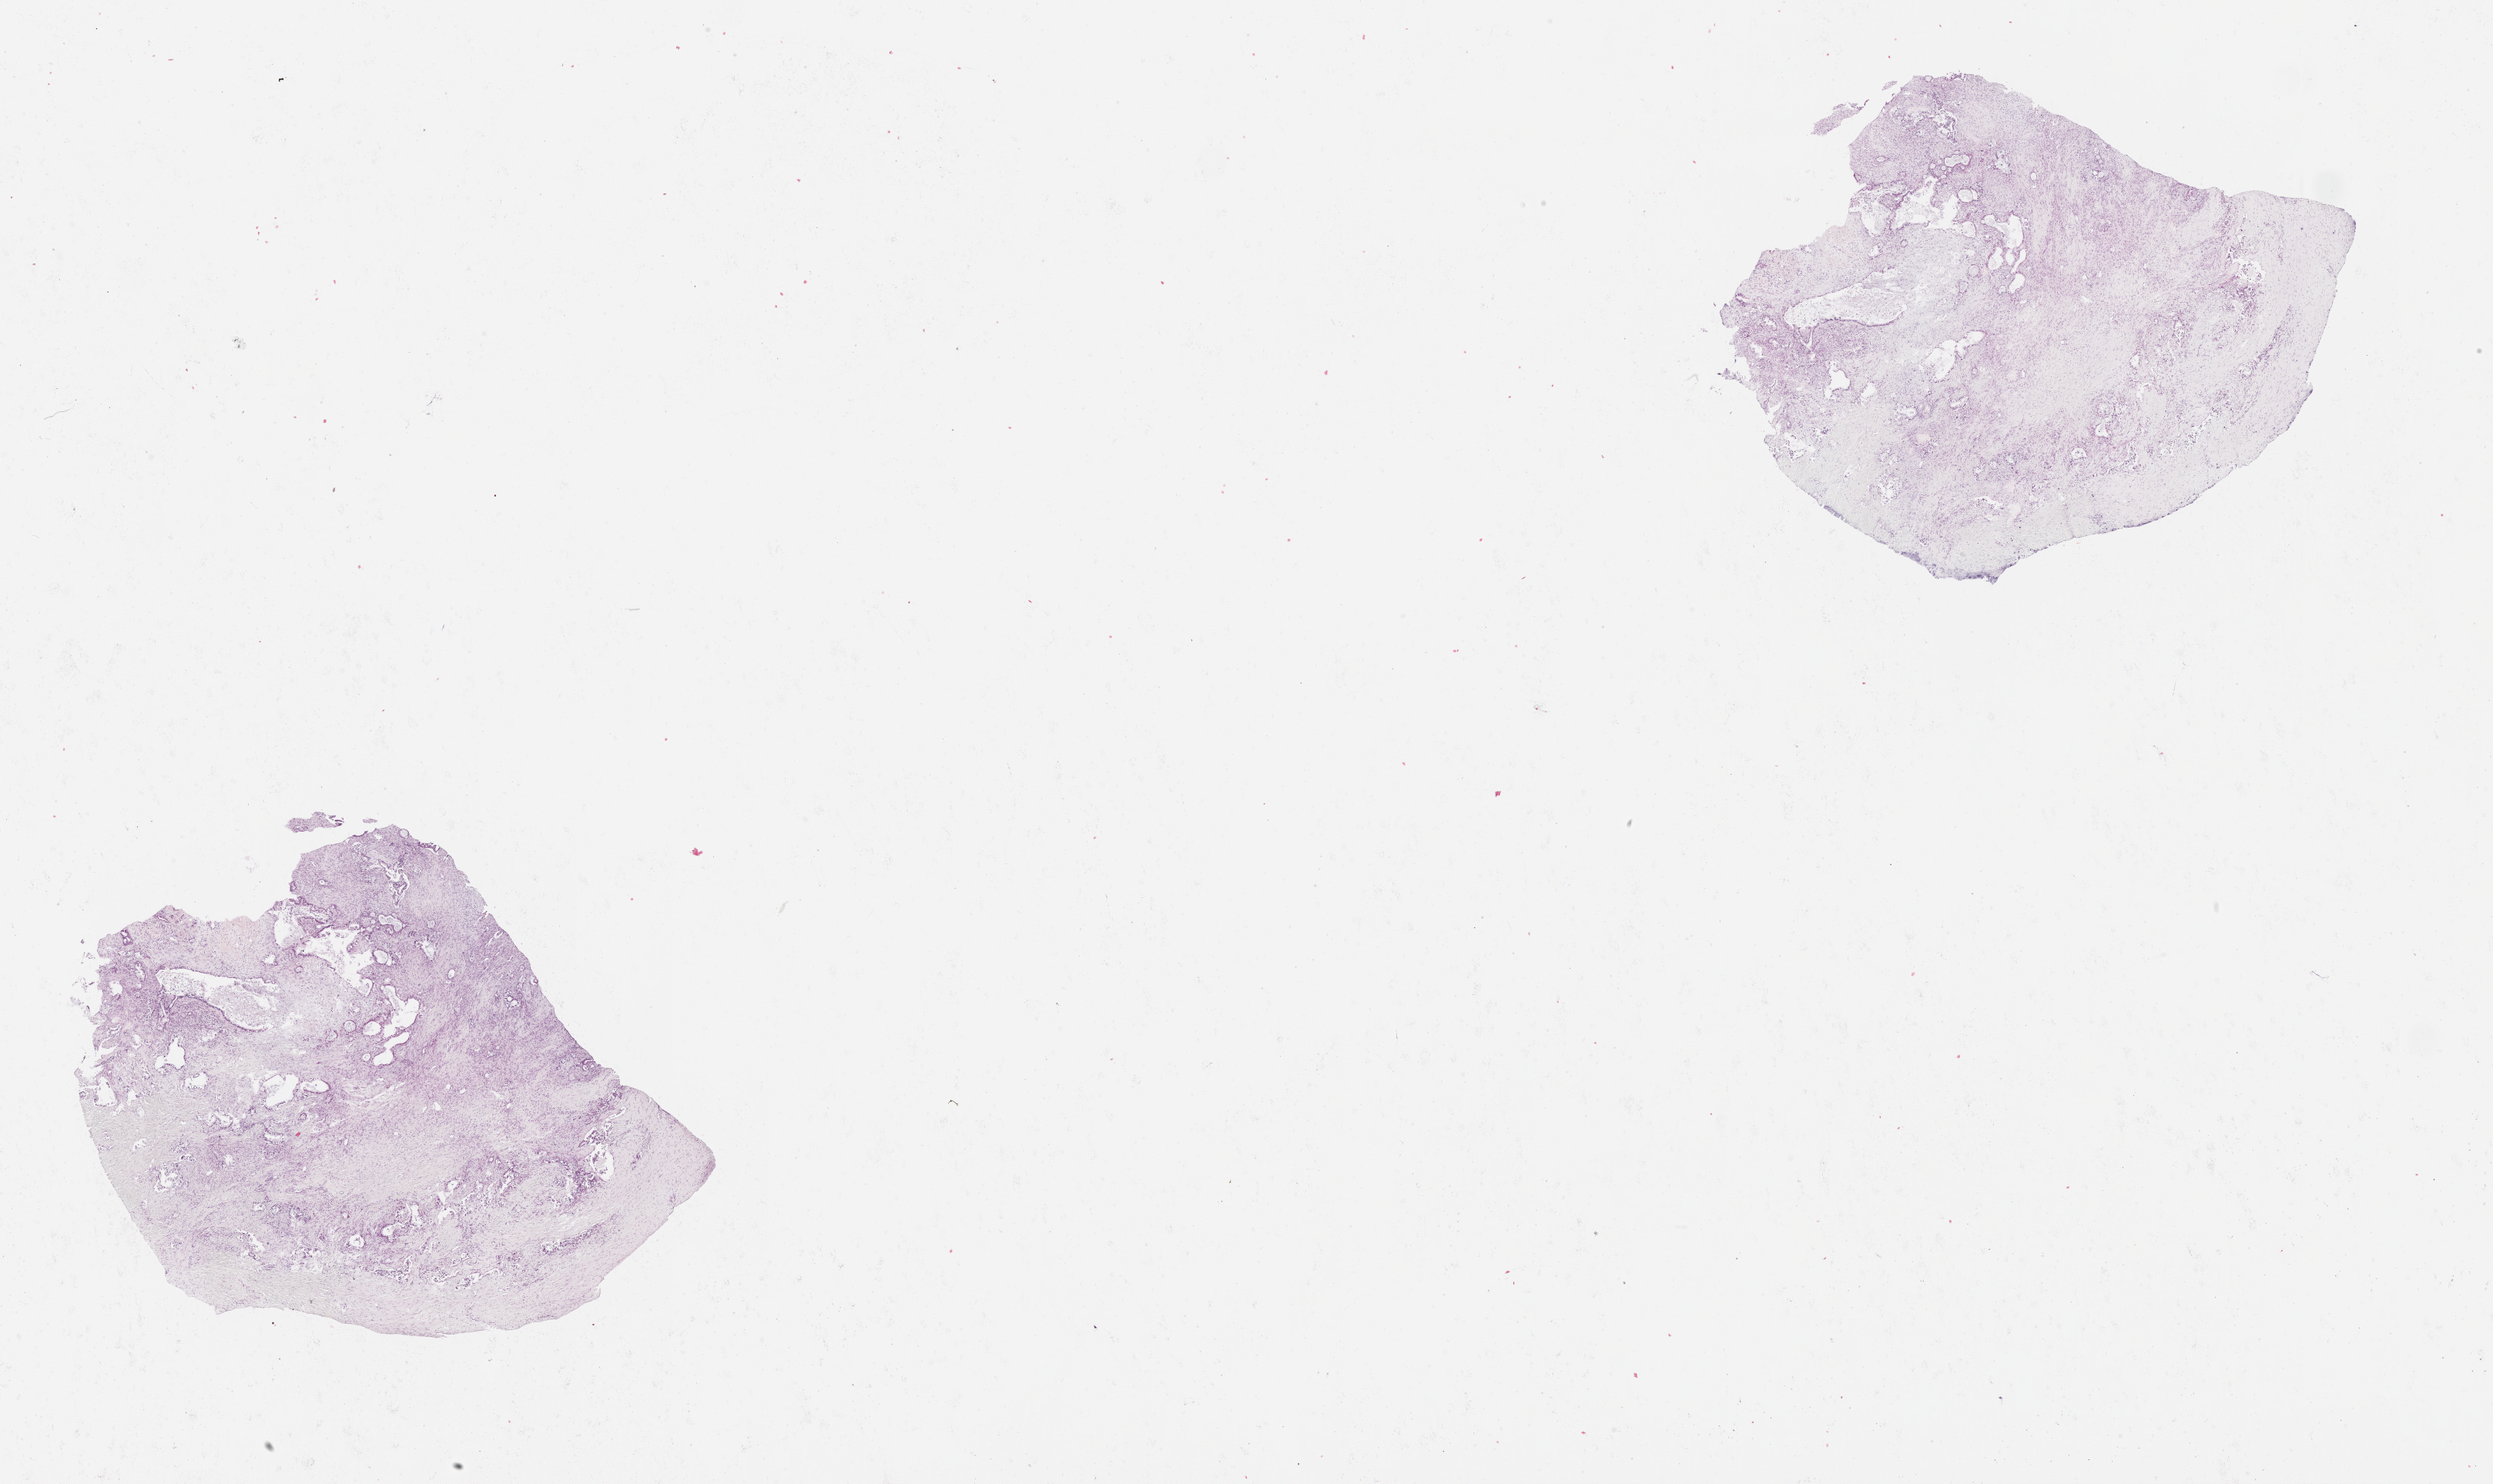
Whole-slide histology image, H&E — whole scanned area (about 26.1 x 15.5 mm, from a 20x scan) shown as a low-resolution overview; tumour tissue sample, sampled site: pancreas. Patient: male, age 63 years. Histologic grade: G2 (moderately differentiated). Pathologist review of this section (percent, as recorded): tumour nuclei 20%, necrosis 0%.
Primary tumour site (as recorded): head. Diagnosis: Infiltrating duct carcinoma, NOS. AJCC pathologic stage: IIB.